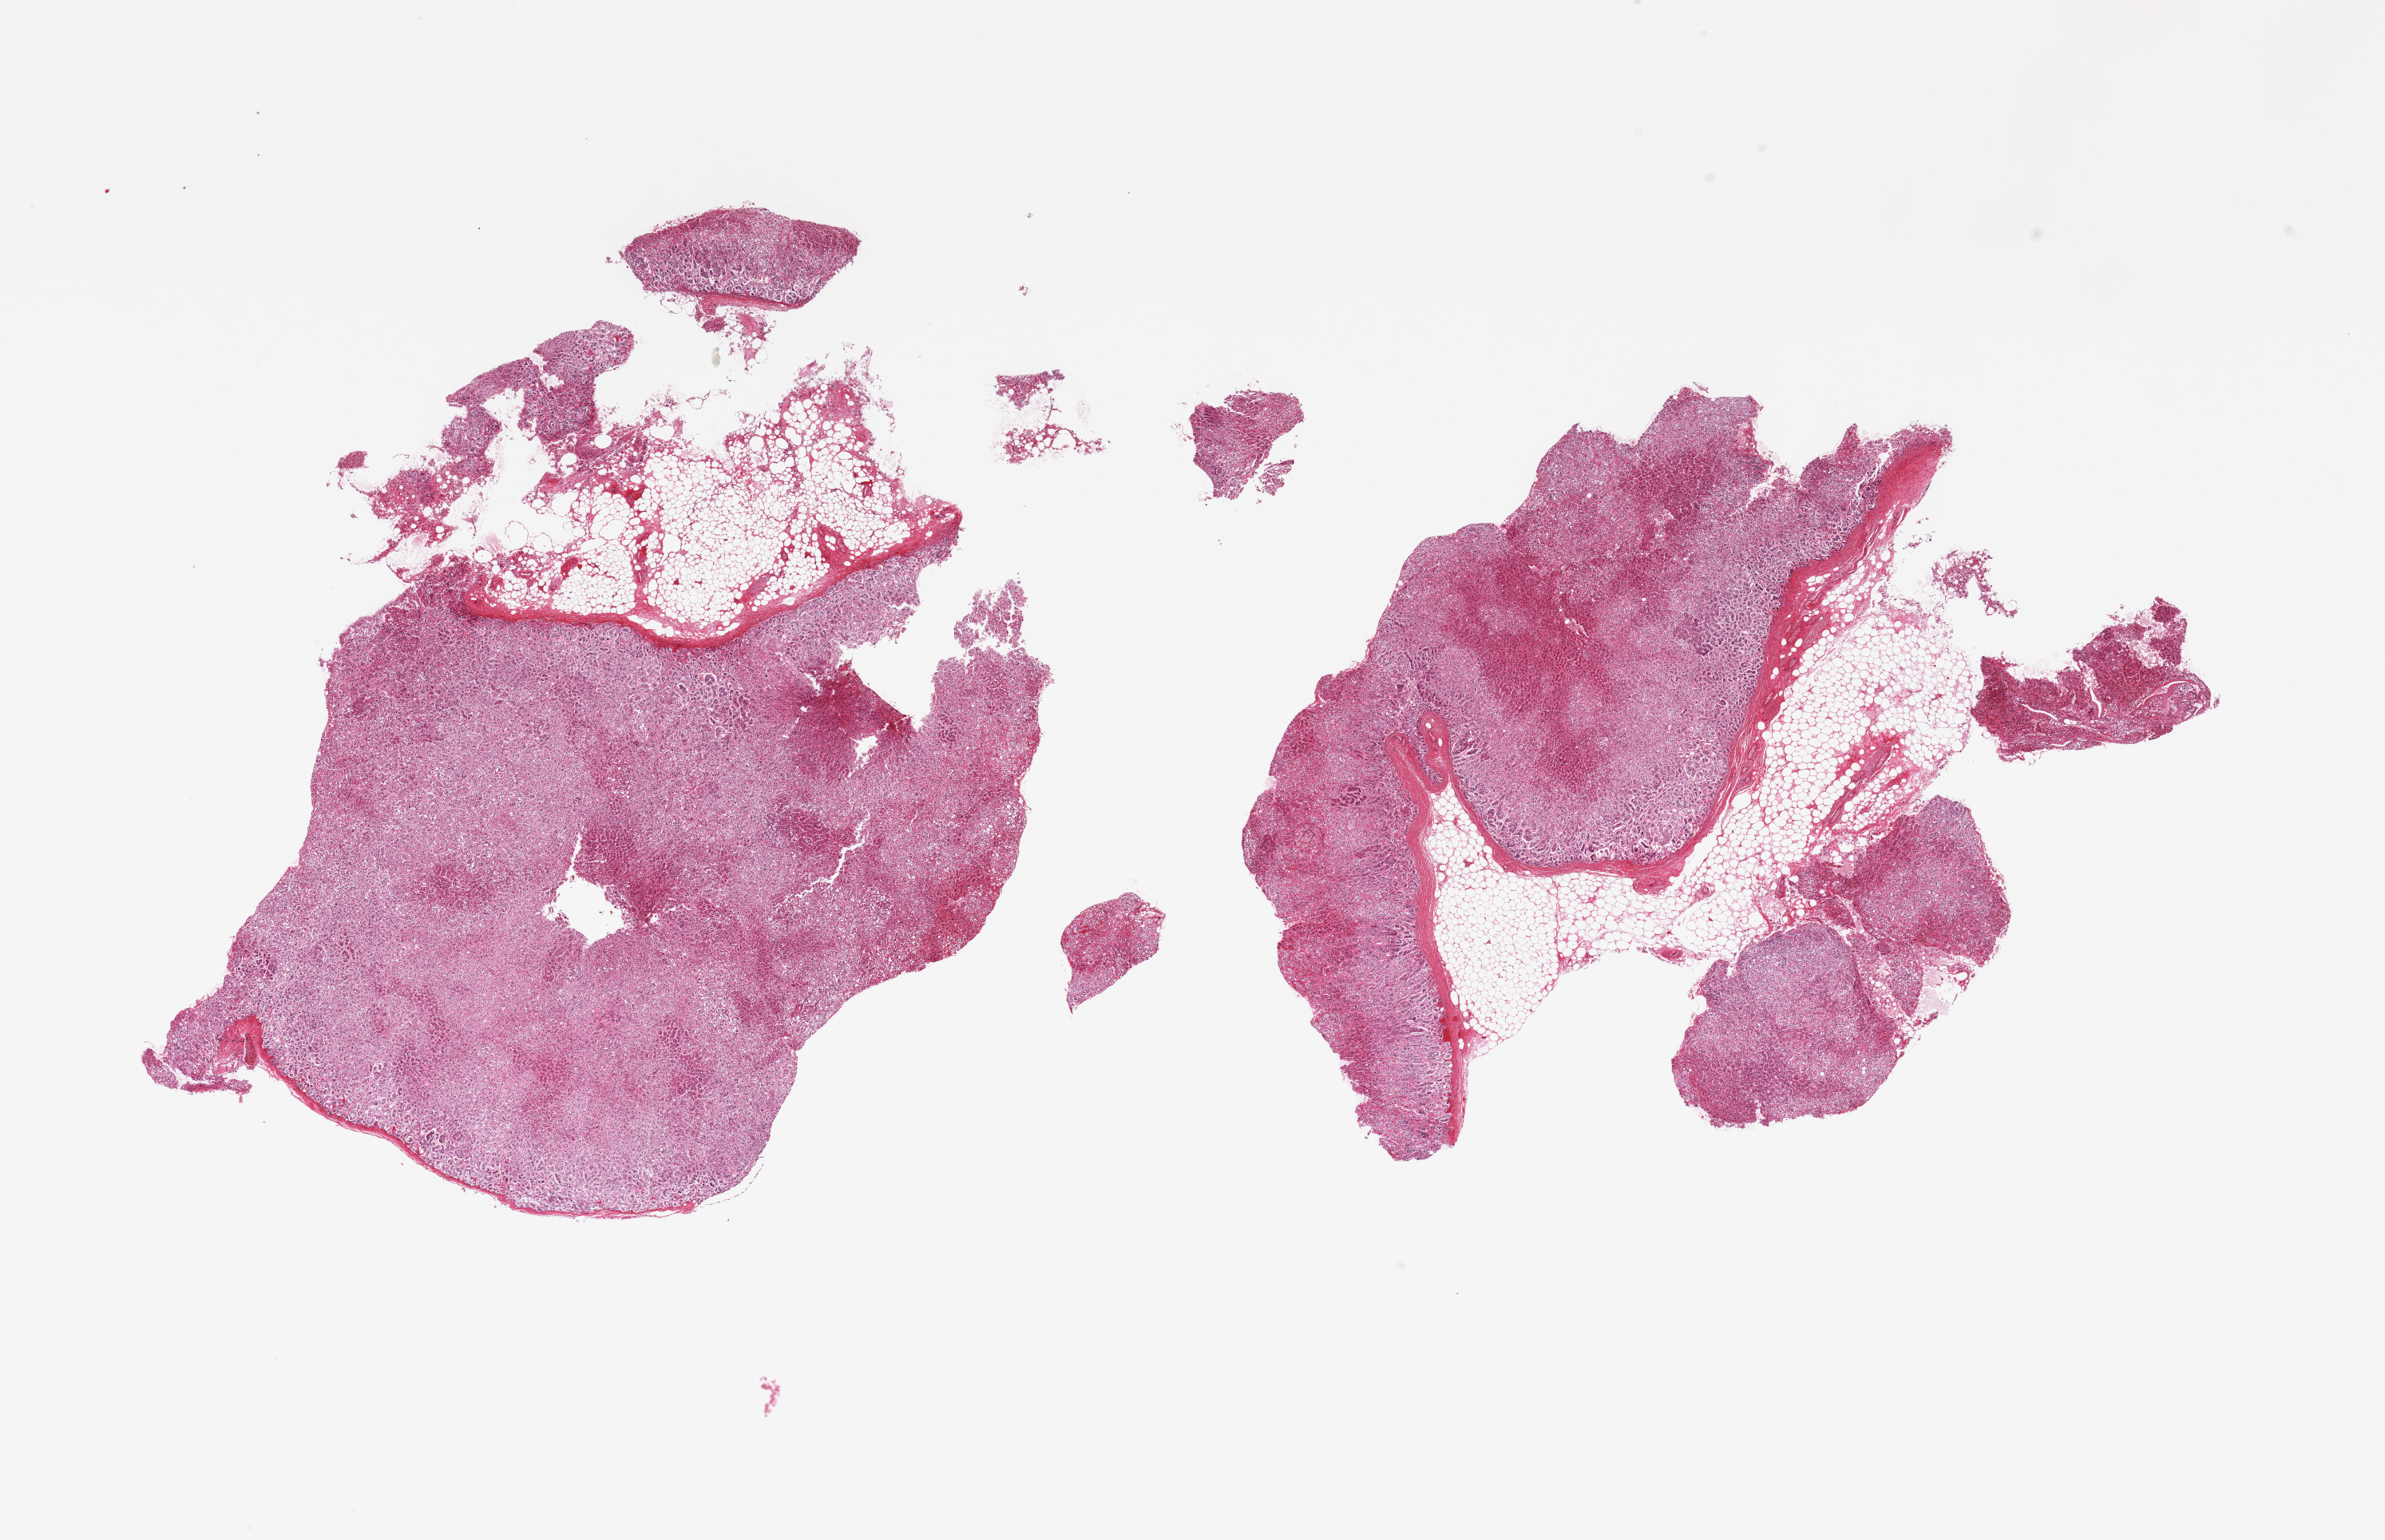
Digitized H&E-stained section, brightfield — whole scanned area (about 23.6 x 15.3 mm) shown as a low-resolution overview; PAXgene-fixed paraffin-embedded (PFPE) section; sampled site (target tissue): adrenal gland; donor tissue sample. Donor: male.
Reviewer comment on this tissue sample: 2 pieces; 20% internal/external fat.